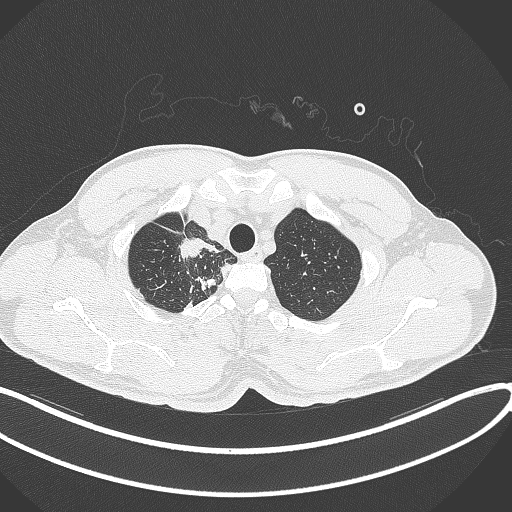
Chest CT, one axial slice. Slice 331 of 391 in the series (ordered by position). Reconstruction kernel B70f. 120 kVp. Lung window (W 1500 / L -600 HU). 1 mm slice thickness. 512 × 512 image matrix, field of view 400 × 400 mm. Patient: male, 48 years. Case-level facts recorded for this patient, not image findings: clinical TNM (as recorded): T1c N1 M1.
Structures marked on this image (bounding box drawn by a radiologist):
- lung tumour (recorded histology: adenocarcinoma): bounding box (x1, y1, x2, y2) in pixels: (175, 233, 204, 262)